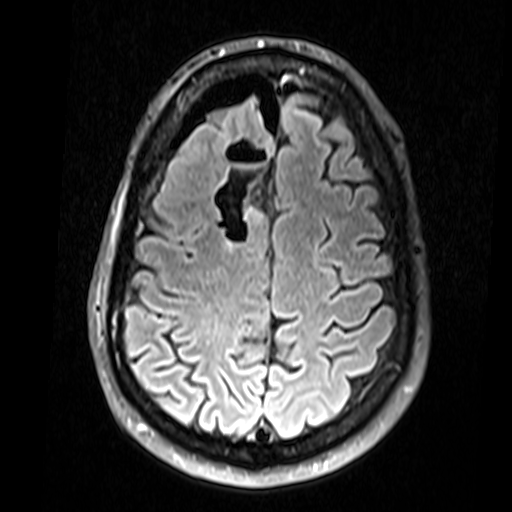
Brain MRI from a brain-tumour surgery series, one axial slice; position 48 of 74 along the scan axis; T2 FLAIR; 512 × 512 image matrix. From the clinical record (not read from this slice): histopathology: Glial fibroma; tumour location: Right Frontal.
Annotated regions visible in this slice (expert manual segmentation):
- residual tumour: bounding box [x1, y1, x2, y2] px = [243, 199, 264, 225]